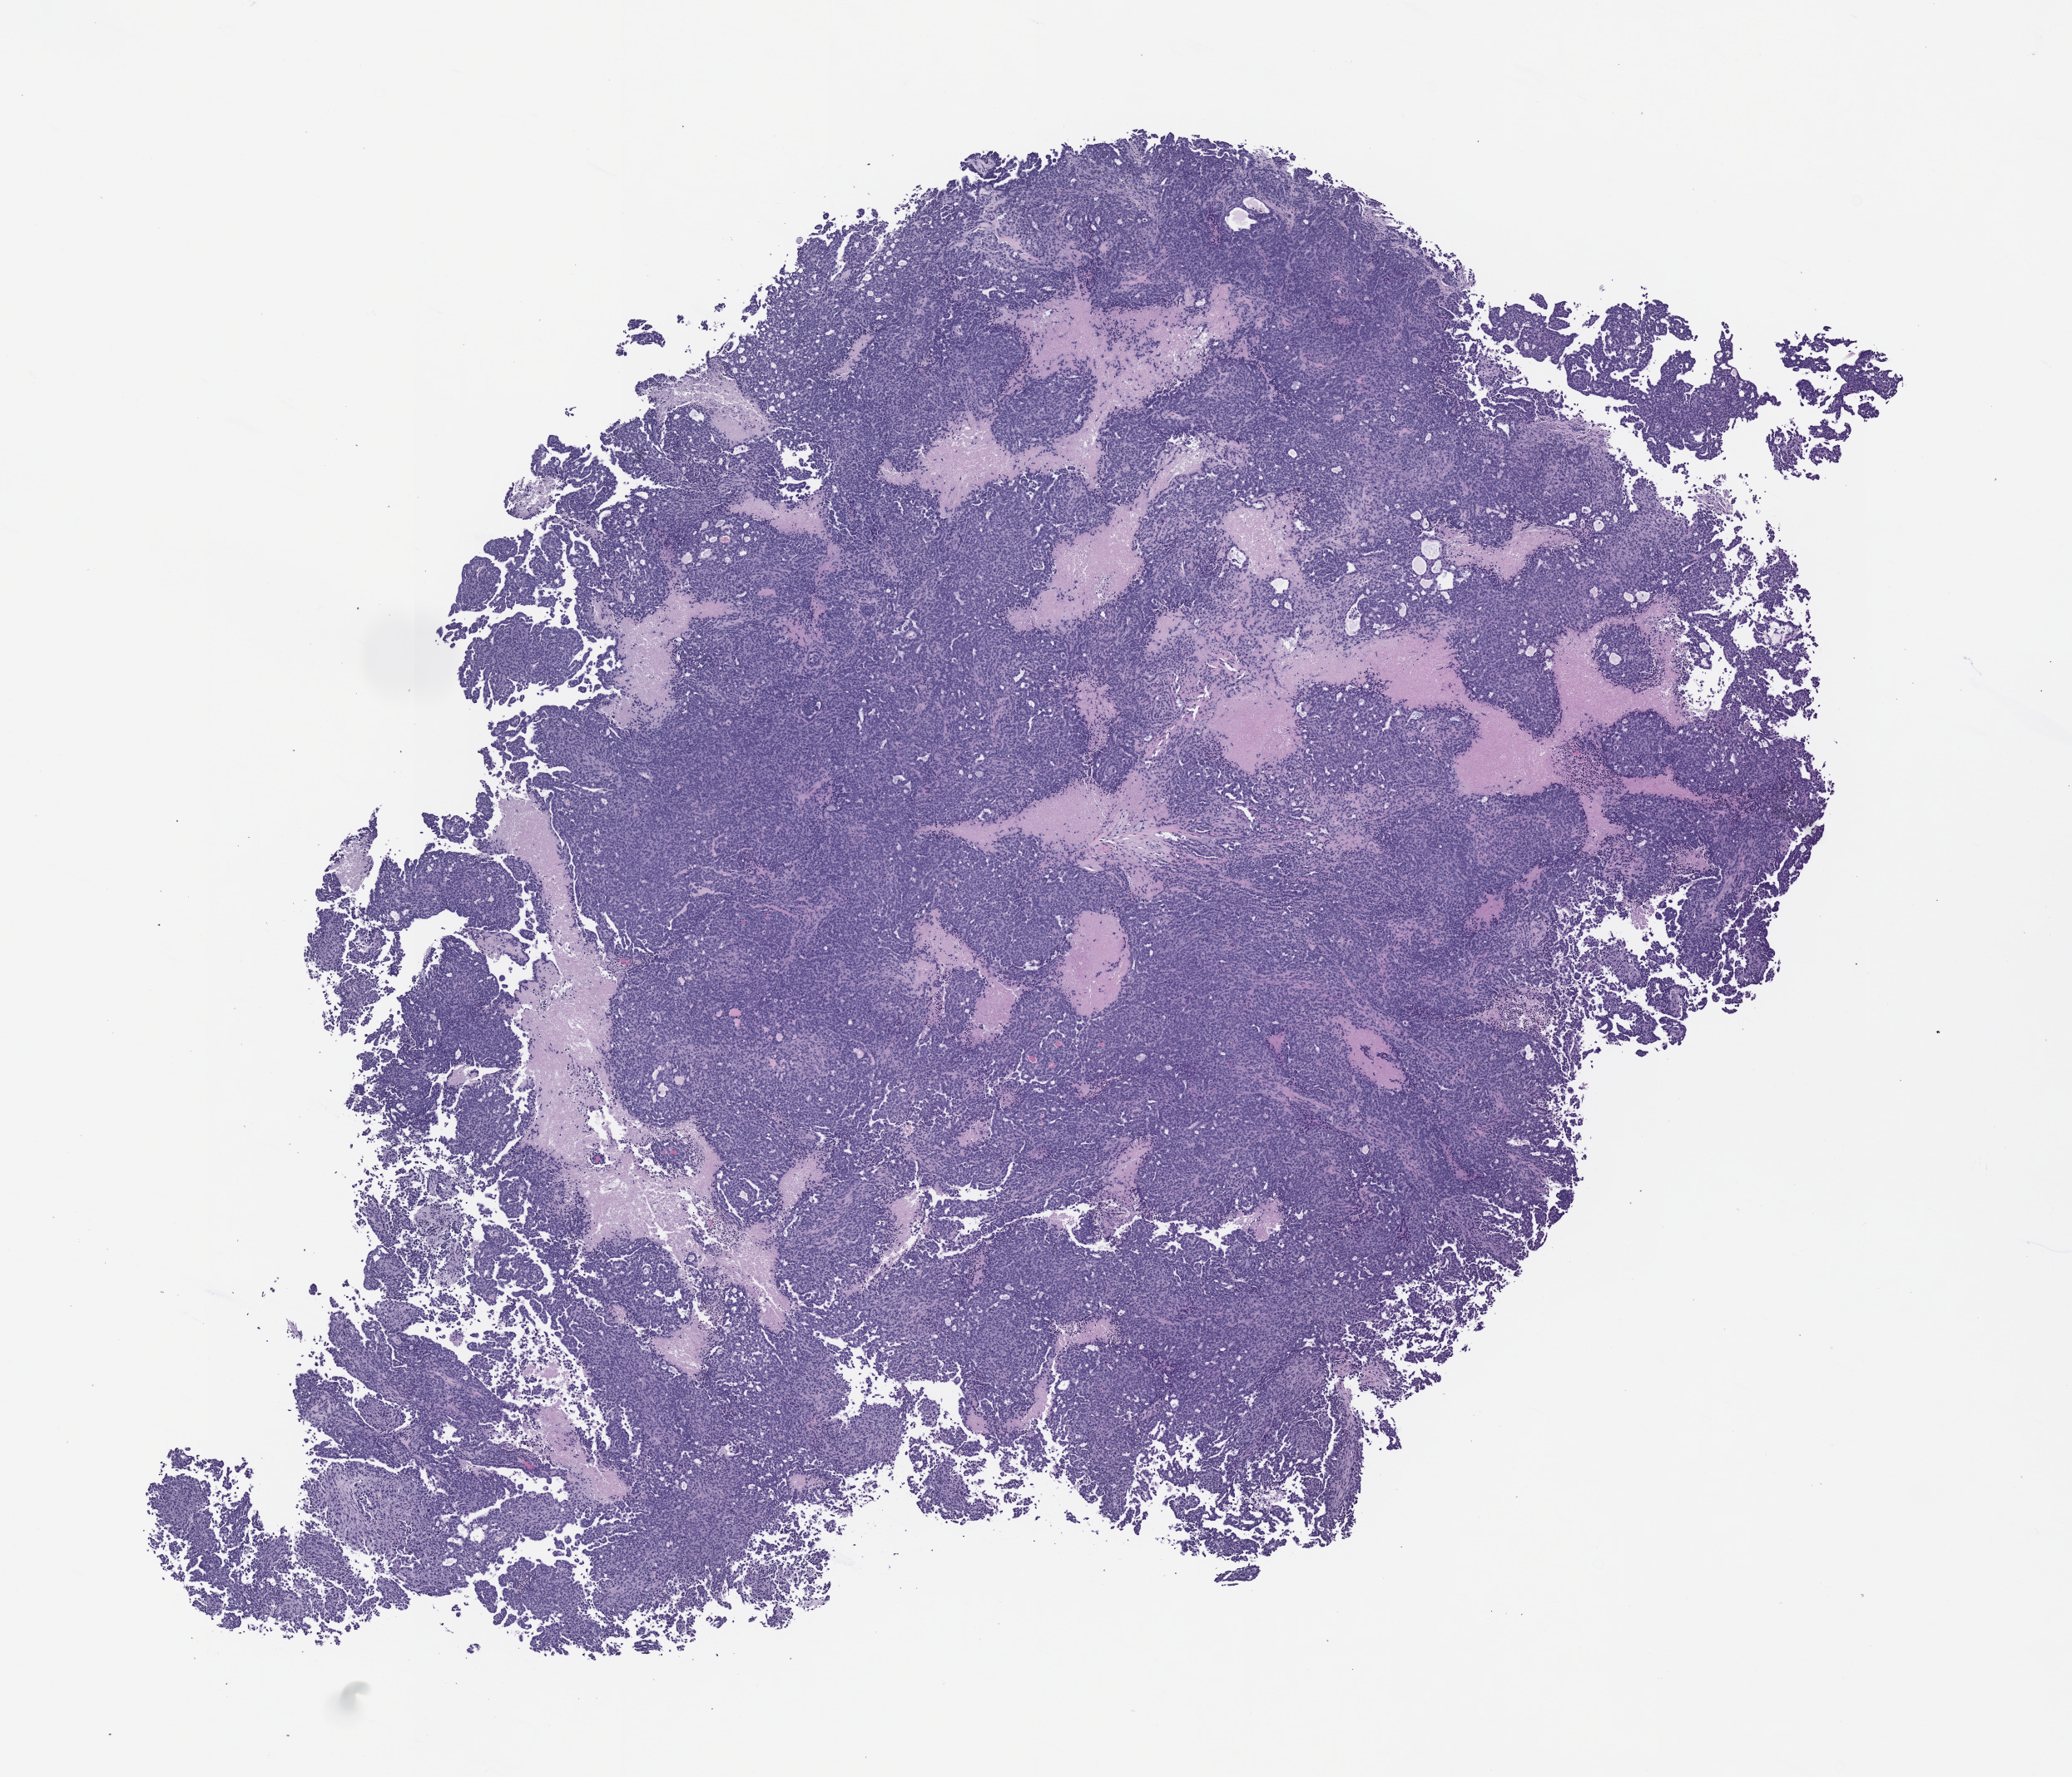
Whole-slide image, hematoxylin and eosin (H&E): patient-derived xenograft (human tumor grown in a mouse), passage 2, shown as a low-resolution overview of the whole scanned area (about 10.0 x 8.6 mm), formalin-fixed, paraffin-embedded (FFPE) tissue.
* originating patient diagnosis: Mesothelial Neoplasm